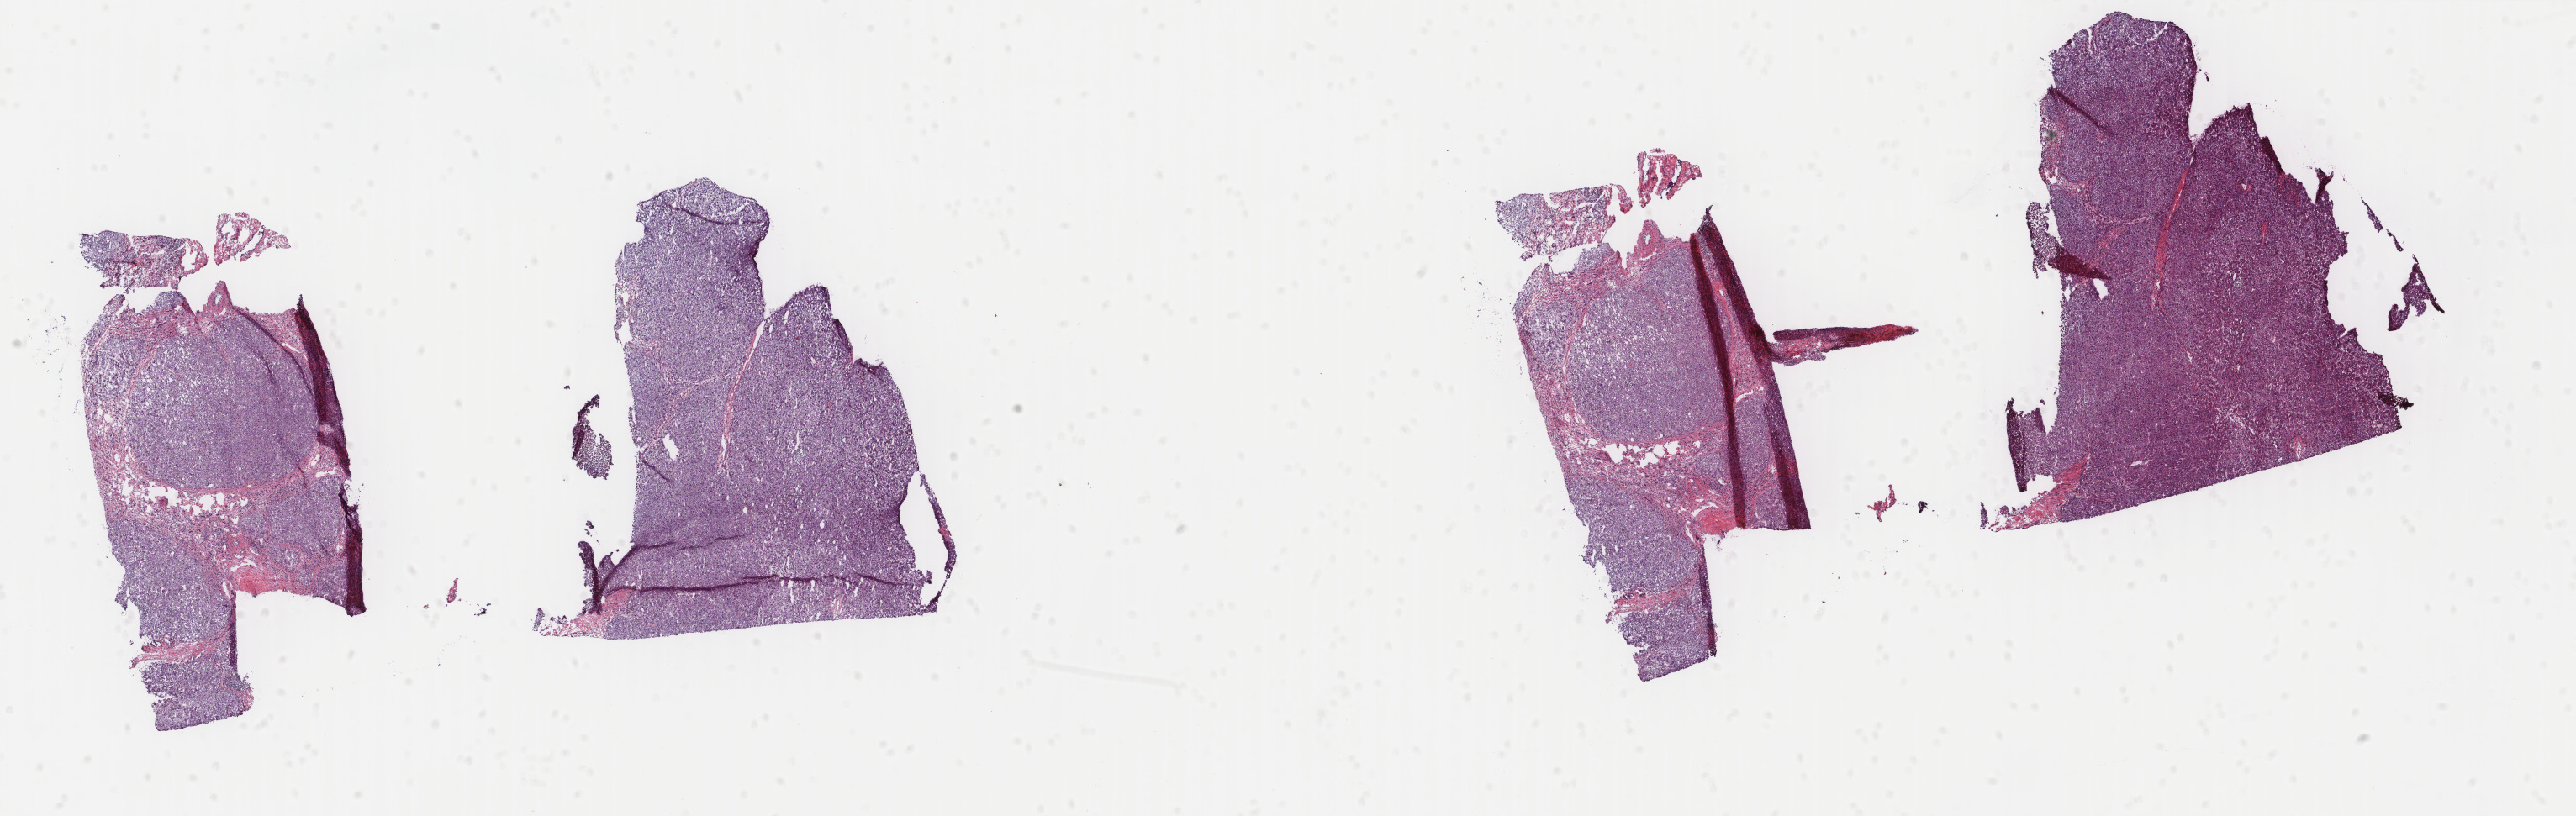
Hematoxylin and eosin (H&E) stained whole-slide image — shown as a low-resolution overview of the whole scanned area (about 24.3 x 7.7 mm, slide scanned at 40x). Frozen section from the top of the tissue portion. Liver, primary tumour sample. Patient: male, age at initial diagnosis 64 years. Histologic grade: G1 (well differentiated). Slide review estimates, as recorded: tumour cells 85%, tumour nuclei 90%, normal cells 0%, stromal cells 14%, necrosis 1%. Inflammatory infiltration, as recorded: lymphocyte infiltration 5%, monocyte infiltration 1%, neutrophil infiltration 1%.
TNM: T1 NX MX. AJCC pathologic stage: I. Diagnosis: Hepatocellular carcinoma, NOS.